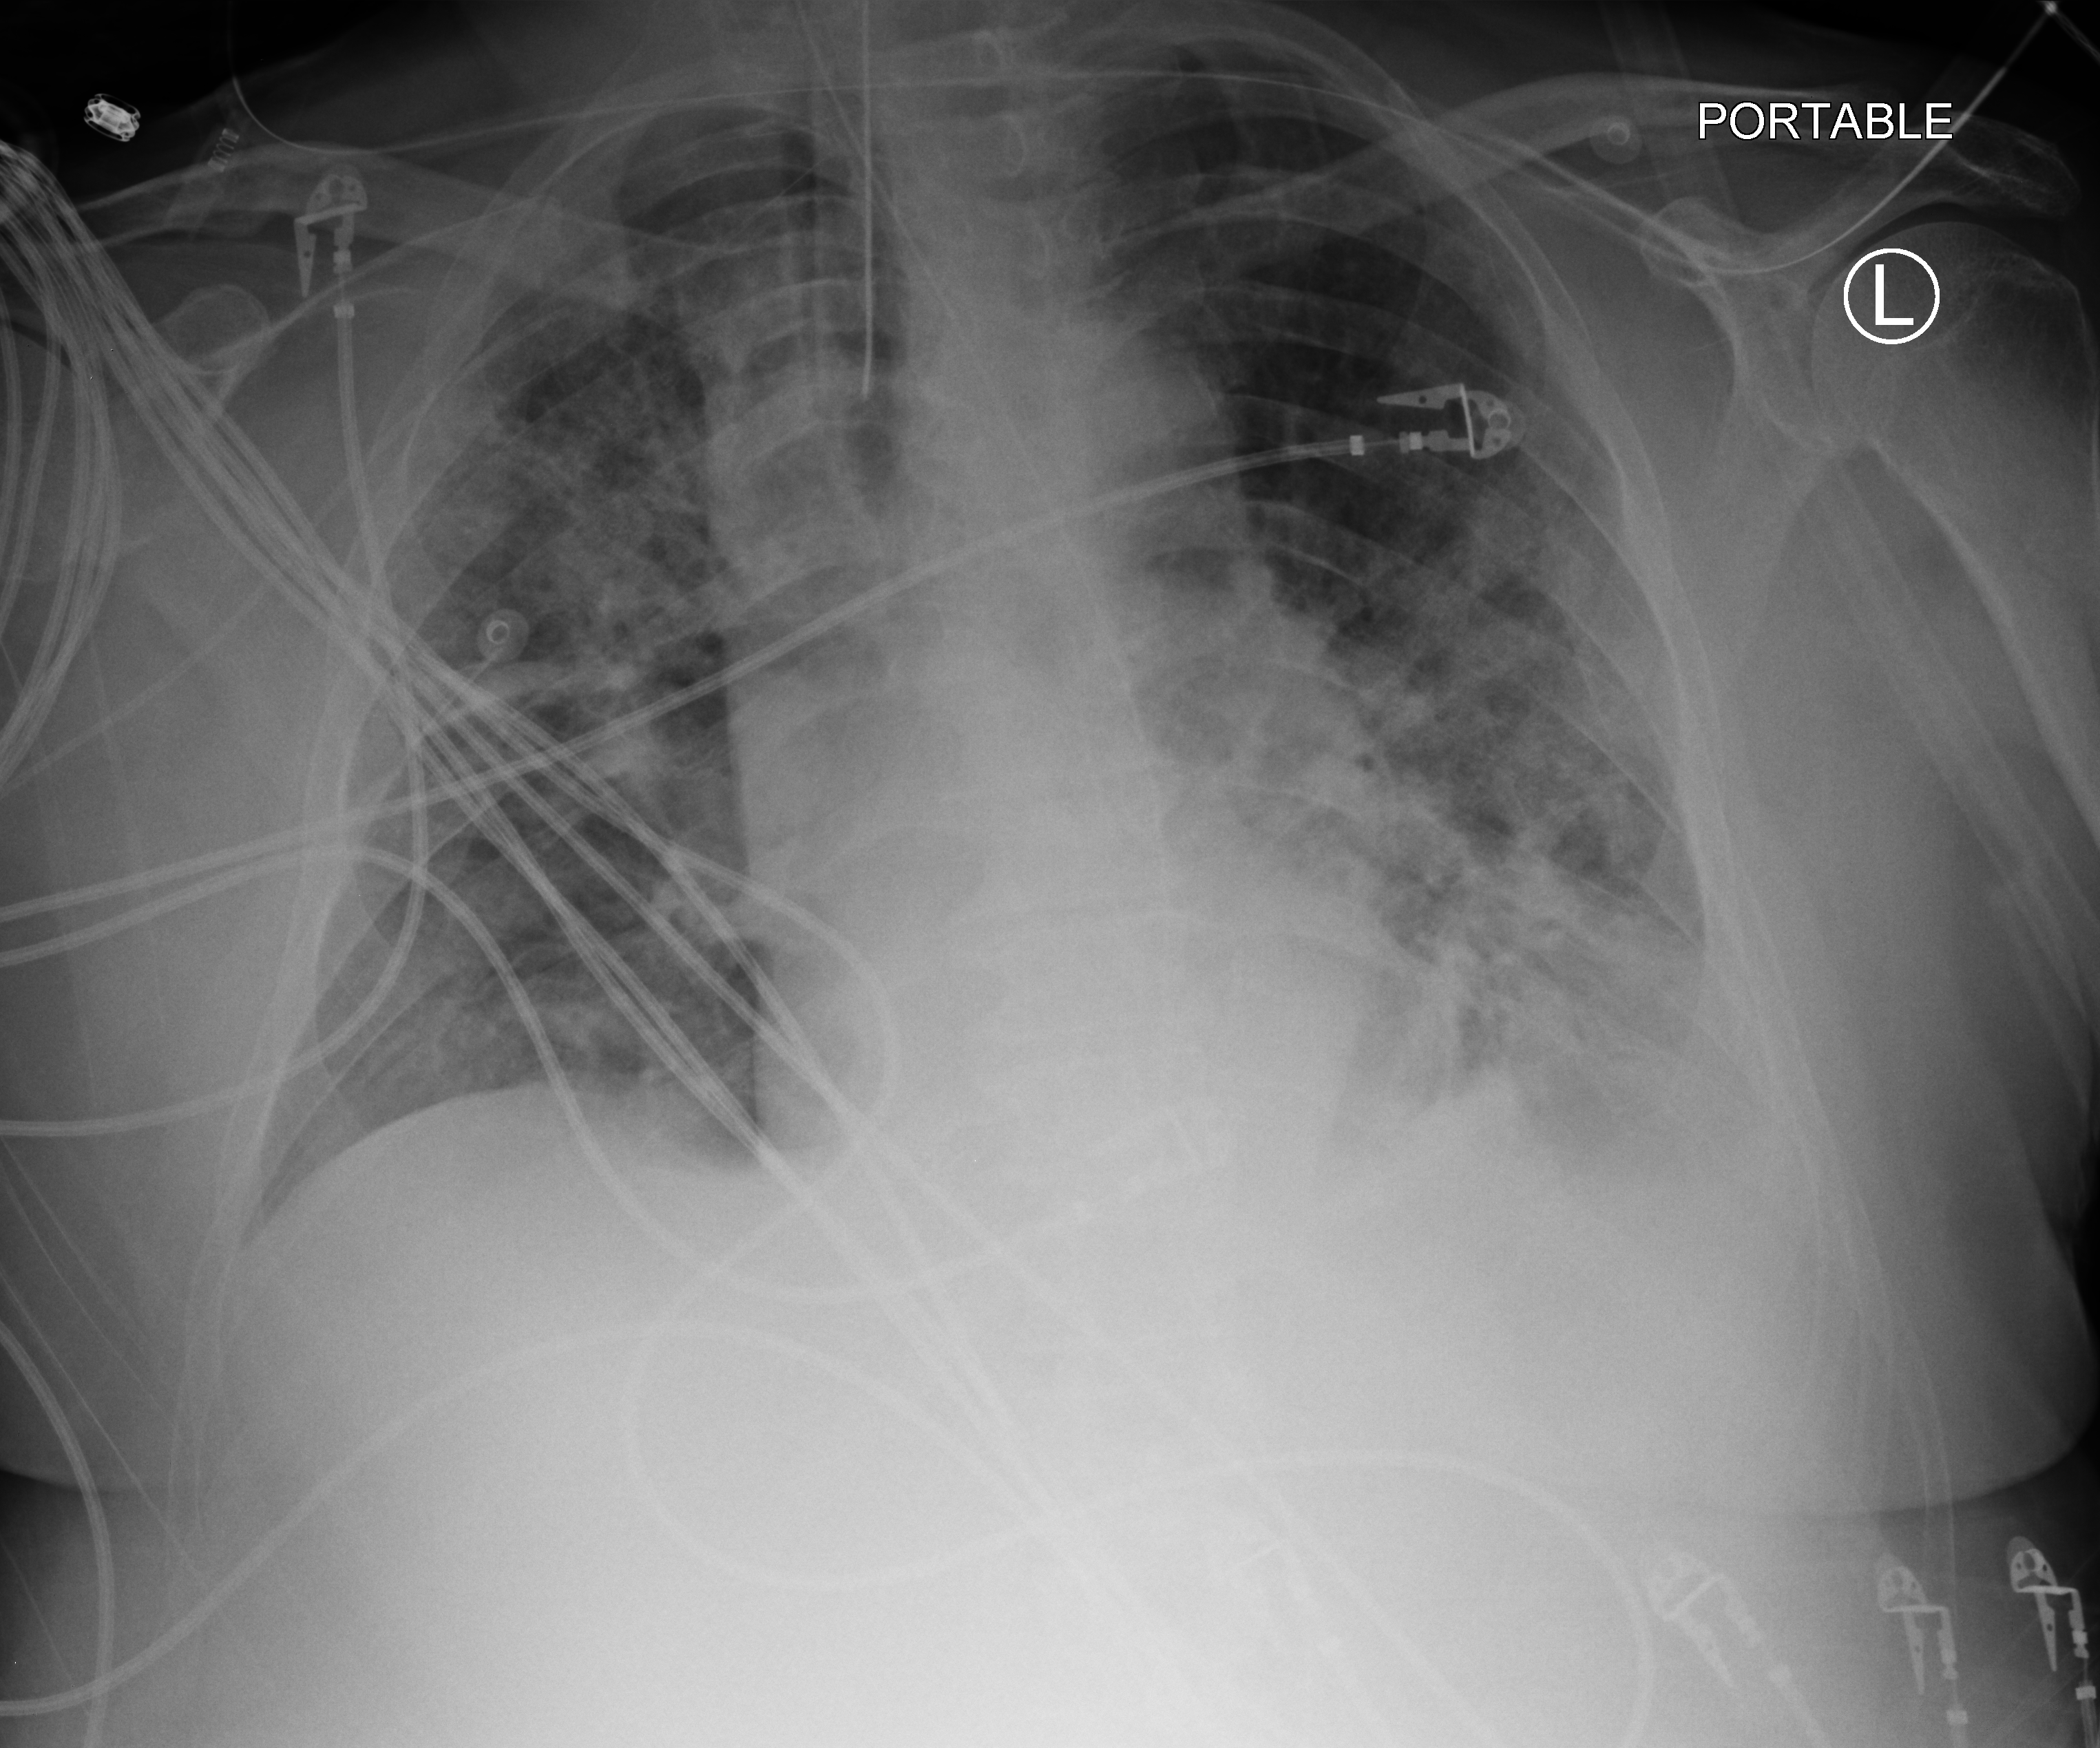
Portable chest radiograph. Male patient hospitalised with COVID-19, age 60–74 years.
From the hospital-stay record, not from the radiograph (when in the stay this image was taken is not recorded):
- admitted to intensive care during this hospital stay: yes